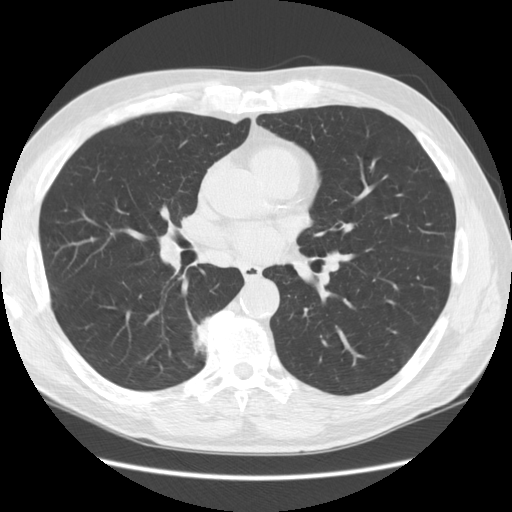
Low-dose screening chest CT, one axial slice. Reconstruction kernel STANDARD. 120 kVp. Lung window (W 1500 / L -600 HU). 2.5 mm slice thickness. 512 × 512 image matrix, field of view 370 × 370 mm.
Structures marked on this image (outlined manually by an expert reader):
- lesion 1 (tumor, lower lobe of right lung): box from (x=196, y=316) to (x=211, y=346) px